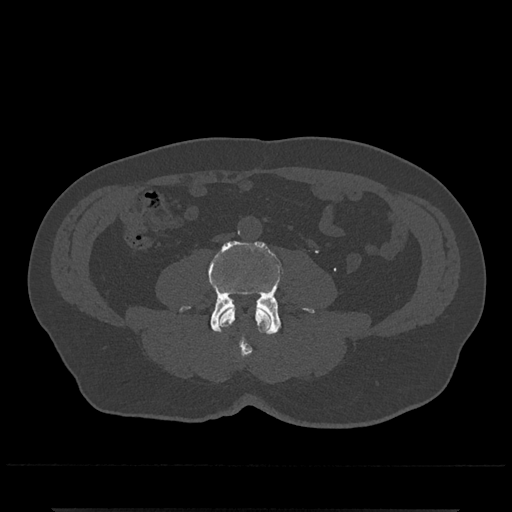
CT including the spine, one axial slice; slice 177 of 797 in the series (ordered by position); reconstruction kernel Br40s/3; 120 kVp; bone window (W 1800 / L 400 HU); 0.5 mm slice thickness; 512 × 512 image matrix, field of view 393 × 393 mm. Patient: male, 67 years. Case-level facts recorded for this patient, not image findings: primary cancer: prostate.
Outlined on this slice (semi-automatic segmentation, software-assisted and operator-edited):
- L3 vertebra: box from (x=219, y=307) to (x=272, y=357) px
- L4 vertebra: (x=180, y=241)–(x=315, y=335)